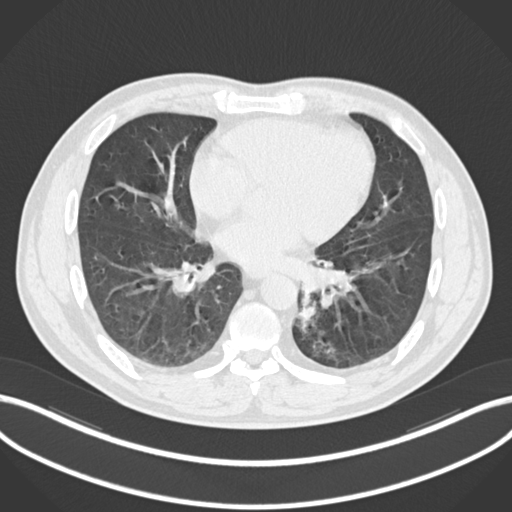
Chest CT, one axial slice. Slice 89 of 223 in the series (ordered by position). Lung window (W 1500 / L -600 HU). 512 × 512 image matrix. Patient: male, 50 years. From the clinical record (not read from this slice): clinical TNM (as recorded): T2a N3 M0.
Annotated regions visible in this slice (rectangle marked by the reading radiologist):
- lung tumour (recorded histology: squamous cell carcinoma): bounding box (x1, y1, x2, y2) in pixels: (295, 293, 319, 336)